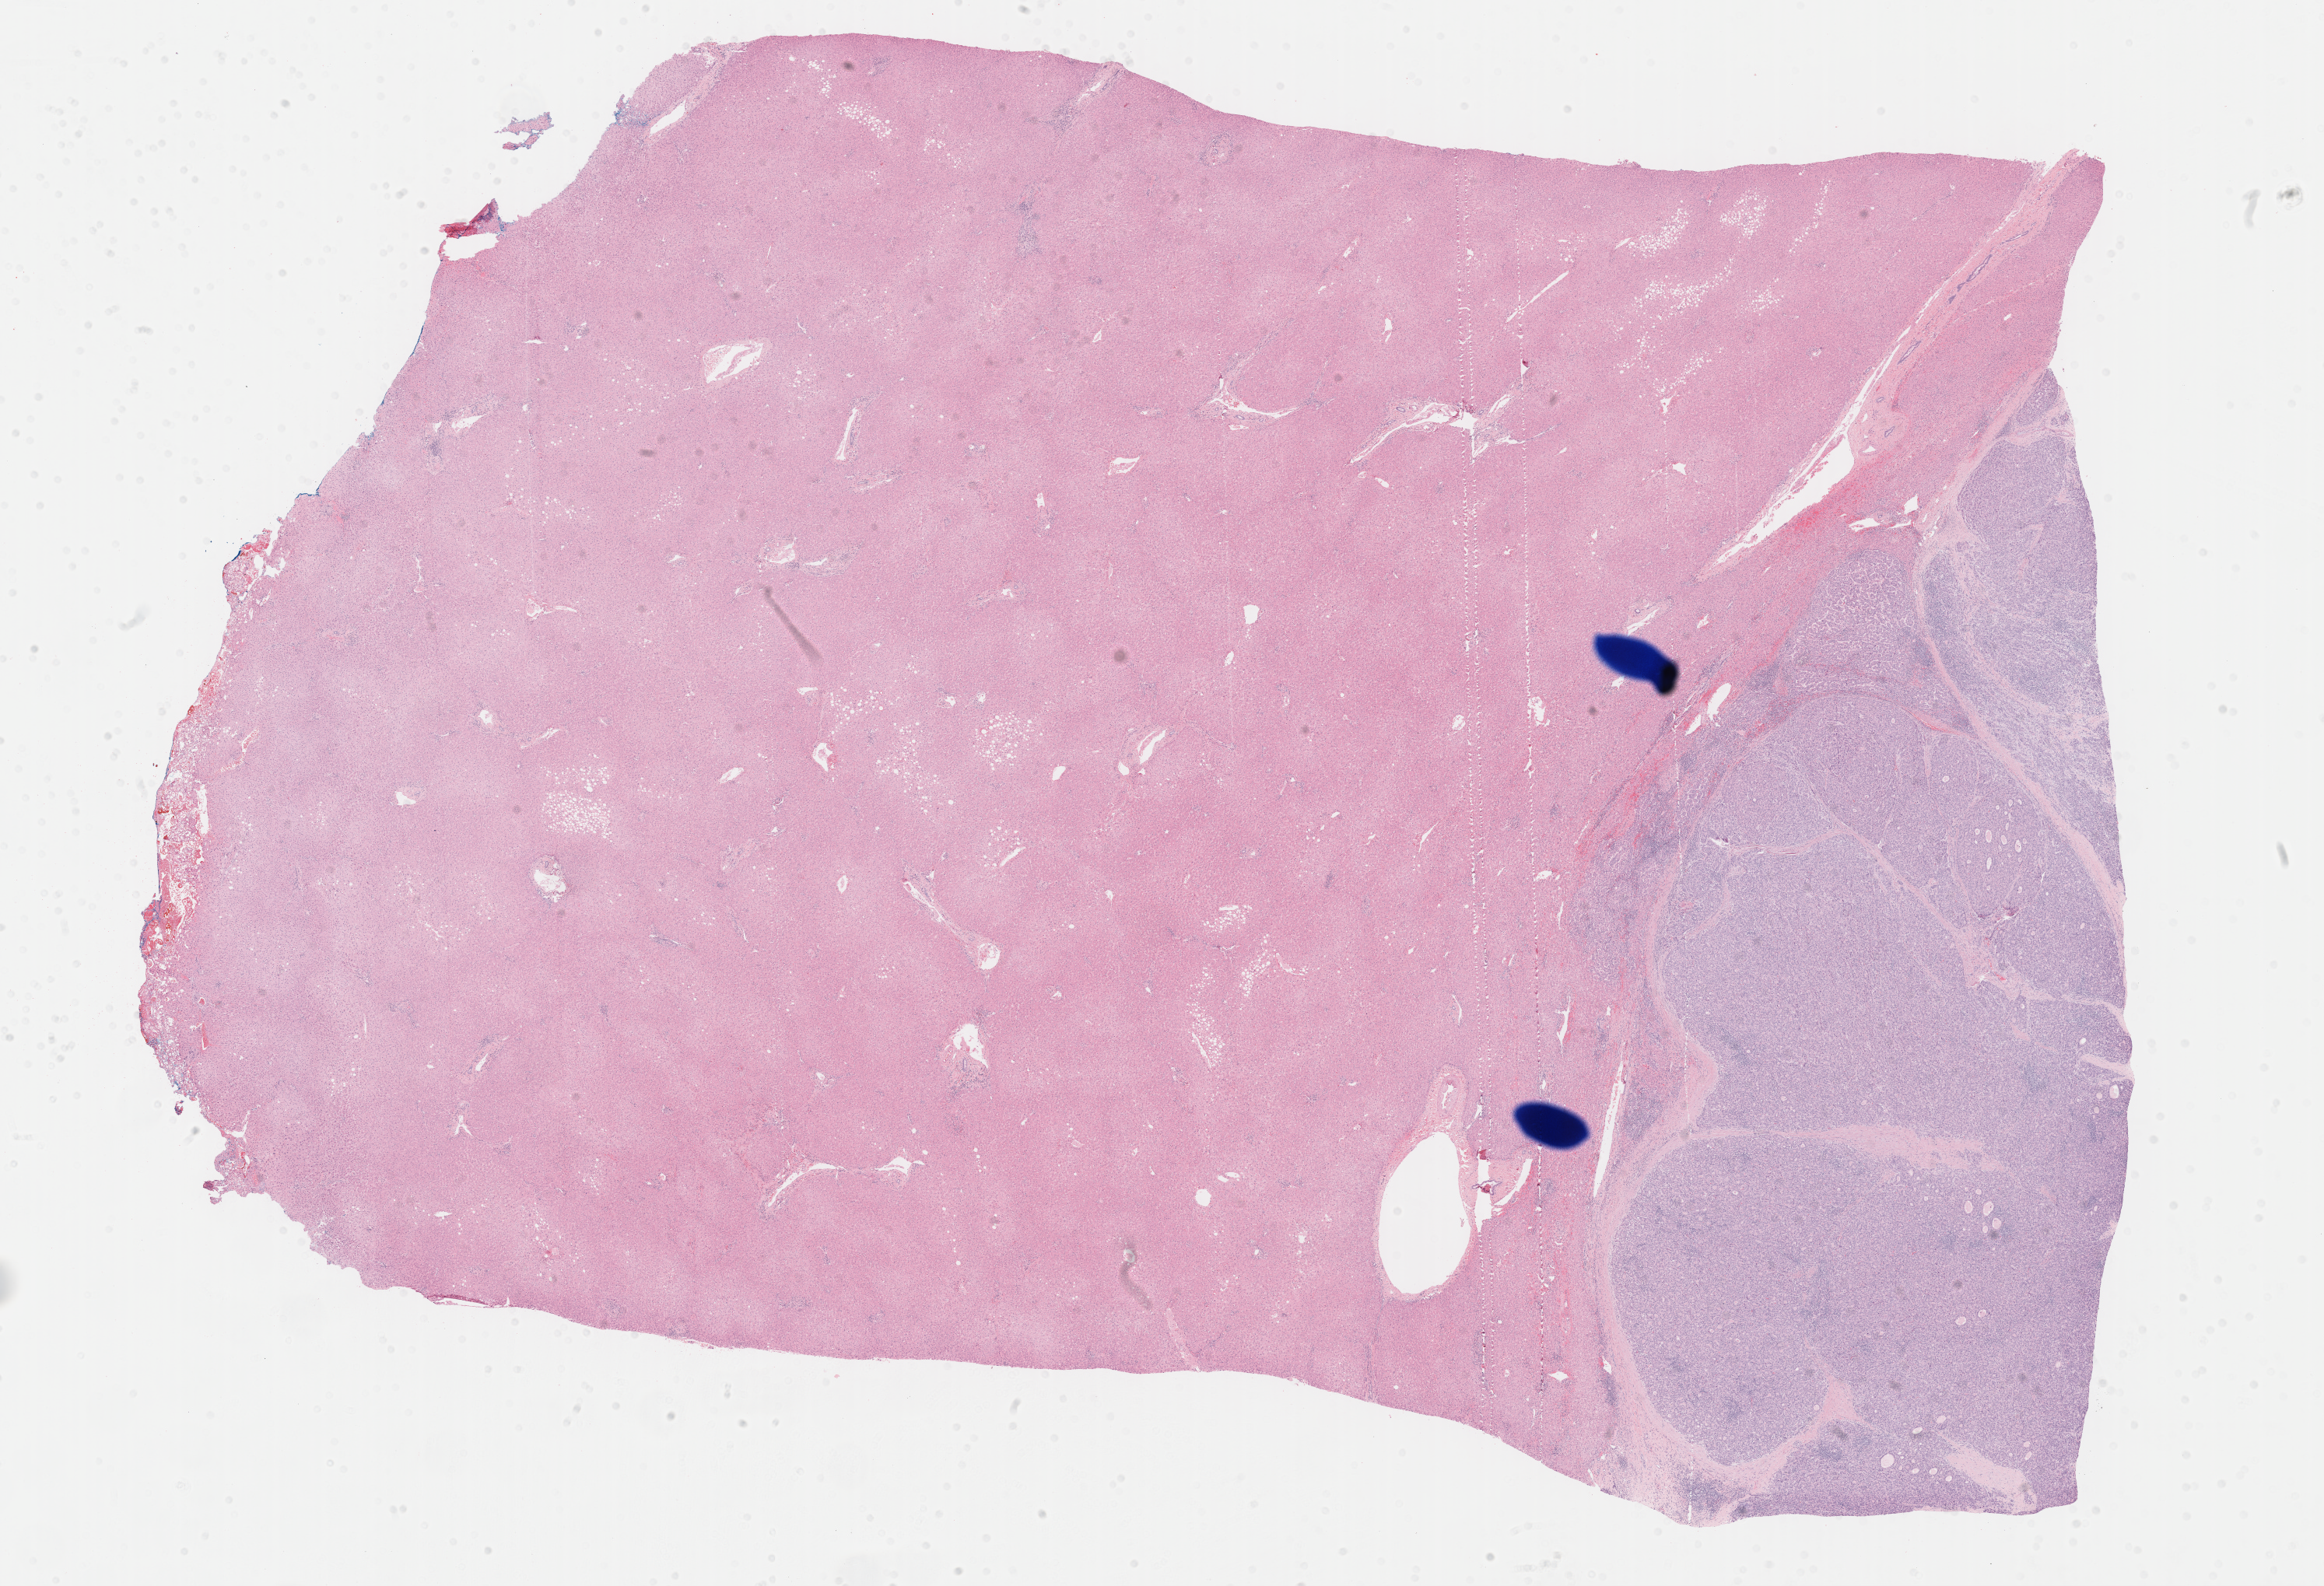
H&E whole-slide image — low-resolution overview of the scanned area, about 24.2 x 16.5 mm (from a 40x scan); formalin-fixed paraffin-embedded (FFPE) diagnostic section; liver, primary tumour sample. Patient: male, age at initial diagnosis 51 years.
Histologic diagnosis: Hepatocellular carcinoma, NOS.